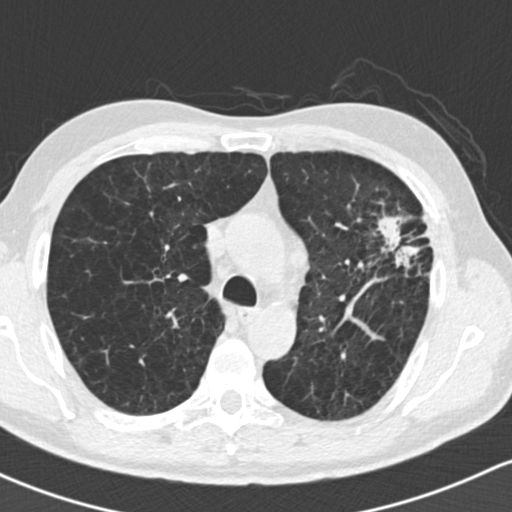
Axial slice from a low-dose chest CT screening exam; baseline screening round; lung window (W 1500 / L -600 HU); standard (soft-tissue) reconstruction kernel (B30f); 120 kVp. Male, age 61 years at enrolment. Former smoker at enrolment.
Lesion marked by an expert reader, bounding box [x1, y1, x2, y2] px = [353, 184, 447, 289]. Reader record for this screening exam (exam-level; its link to the box is not recorded): non-calcified nodule or mass ≥4 mm, left upper lobe, 35 × 35 mm, spiculated (stellate) margins, soft tissue attenuation.